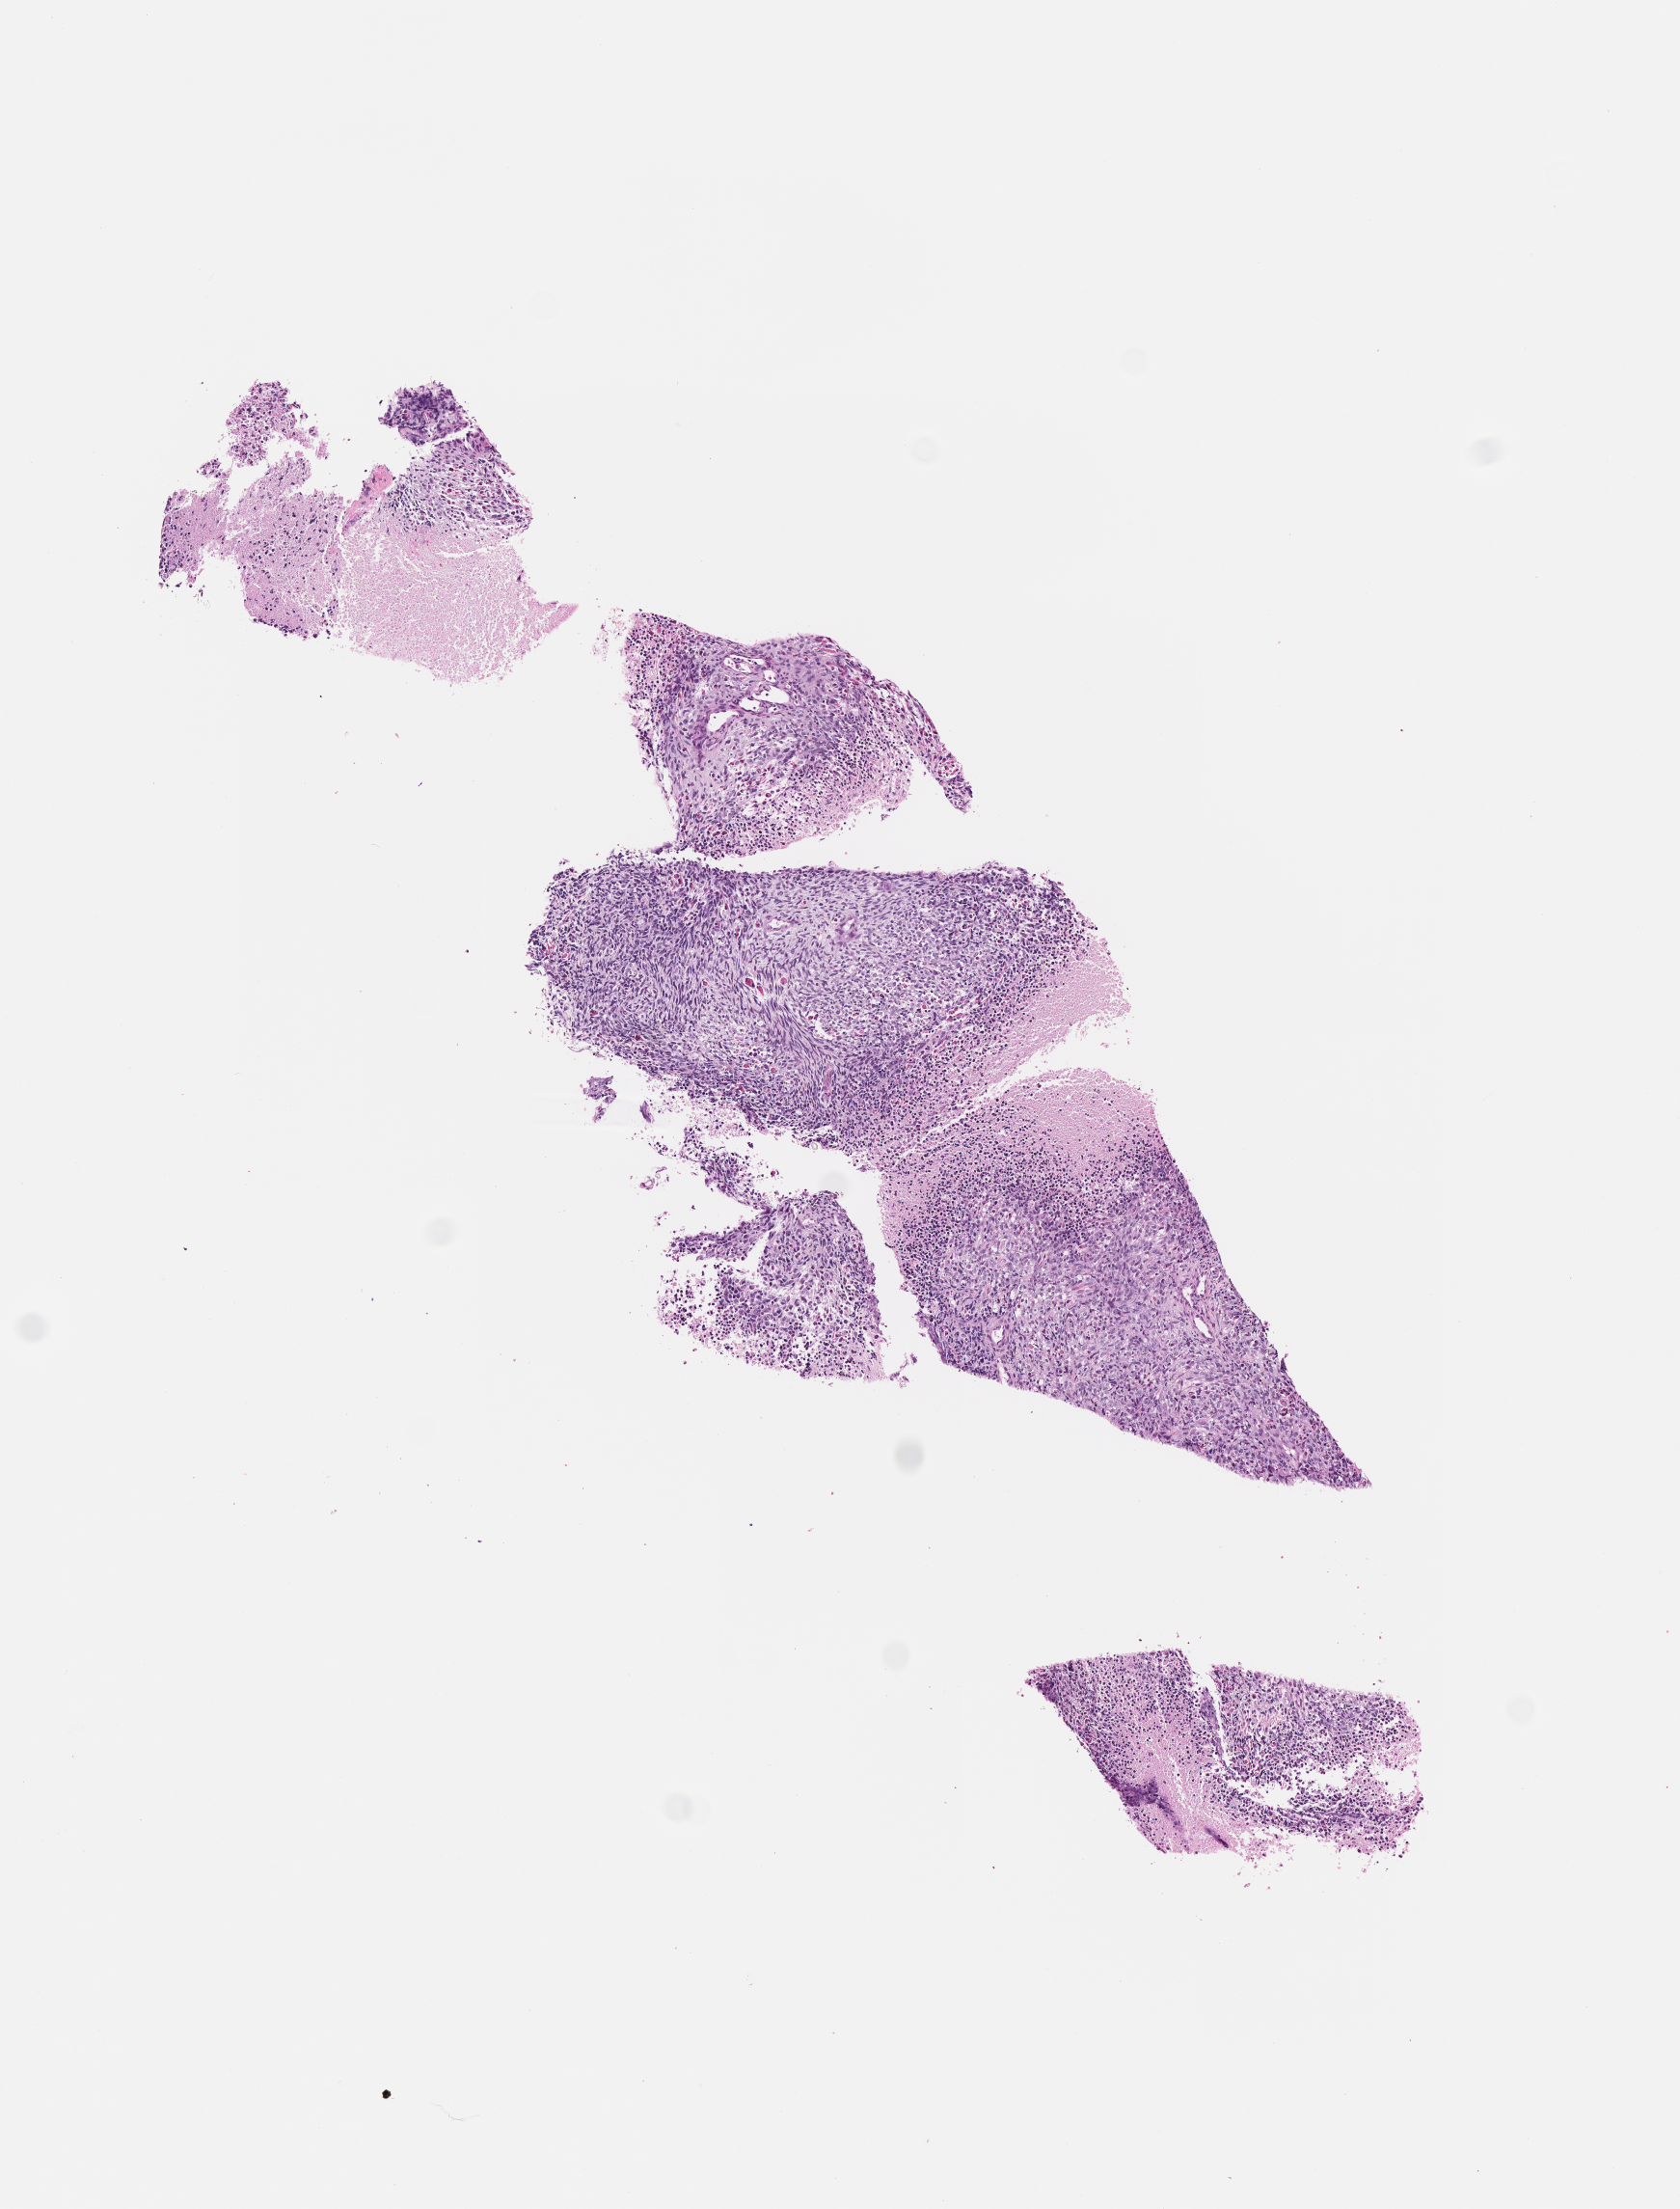
Whole-slide image, haematoxylin and eosin stain of tumor tissue, a low-resolution overview of the entire scanned area, about 3.5 x 4.6 mm. Formalin-fixed, paraffin-embedded (FFPE) tissue. Site: pelvis (prostate). Male patient, age at diagnosis 4.1 years.
Primary site (case record): bladder. Stage (as recorded): 3. Metastatic status at presentation (as recorded): non-metastatic (confirmed). Diagnosis: rhabdomyosarcoma; histological classification: embryonal rhabdomyosarcoma.